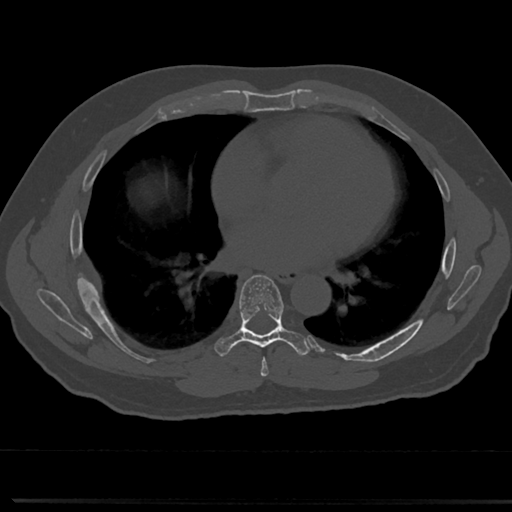
CT including the spine, one axial slice. Slice 410 of 817 in the series (ordered by position). Reconstruction kernel Br40s/3. Bone window (W 1800 / L 400 HU). 0.5 mm slice thickness. 512 × 512 image matrix, field of view 355 × 355 mm. Male patient, age 61 years. Case-level facts recorded for this patient, not image findings: primary cancer: prostate.
Outlined on this slice (semi-automatic segmentation, software-assisted and operator-edited):
- T6 vertebra: bounding box (x1, y1, x2, y2) in pixels: (255, 338, 319, 368)
- T7 vertebra: (216, 275, 307, 357)